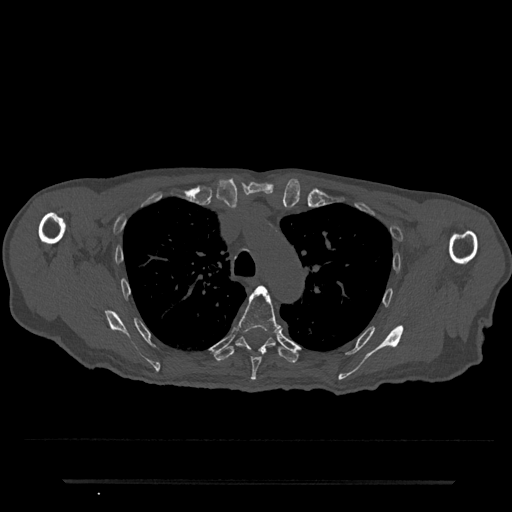
CT including the spine, one axial slice; slice 562 of 797 in the series (ordered by position); 120 kVp; bone window (W 1800 / L 400 HU); 512 × 512 image matrix, field of view 427 × 427 mm. Male patient, age 74 years. From the clinical record (not read from this slice): primary cancer: prostate.
Annotated regions visible in this slice (semi-automatically segmented with operator editing):
- T5 vertebra: box from (x=237, y=286) to (x=282, y=381) px
- T6 vertebra: (x=214, y=337)–(x=298, y=364)